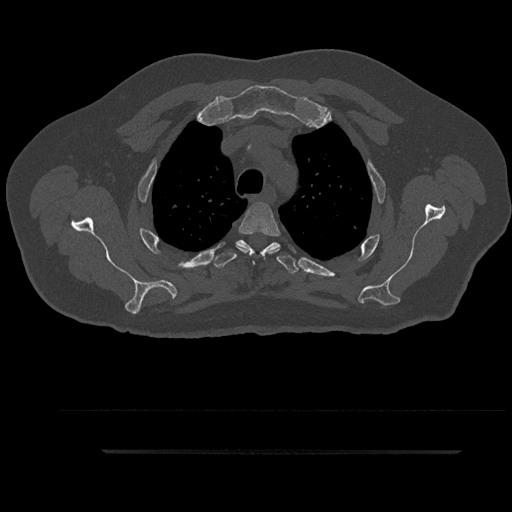
CT including the spine, one axial slice. Slice 700 of 797 in the series (ordered by position). Reconstruction kernel Br40s/3. Bone window (W 1800 / L 400 HU). 0.5 mm slice thickness. 512 × 512 image matrix, field of view 432 × 432 mm. Patient: male, 63 years. Case-level facts recorded for this patient, not image findings: primary cancer: renal; vertebrae with lytic lesions (as recorded): T8.
Outlined on this slice (semi-automatically segmented with operator editing):
- T3 vertebra: bounding box [x1, y1, x2, y2] px = [236, 201, 280, 255]
- T4 vertebra: [211, 240, 299, 274]